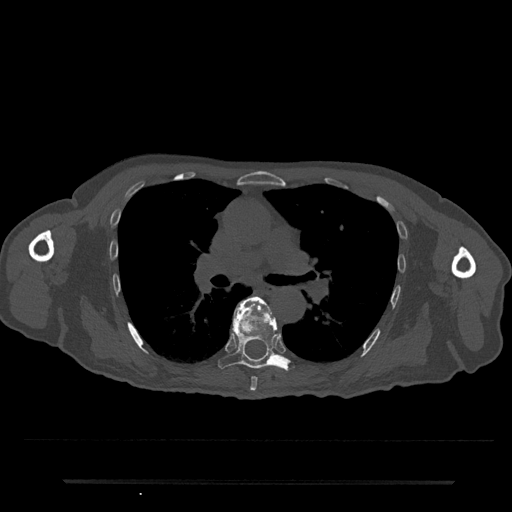
CT including the spine, one axial slice. Position 493 of 797 along the scan axis. Reconstruction kernel Br40s/3. 120 kVp. Bone window (W 1800 / L 400 HU). 0.5 mm slice thickness. 512 × 512 image matrix. Male patient, age 74 years. From the clinical record (not read from this slice): primary cancer: prostate.
Annotated regions visible in this slice (semi-automatically segmented with operator editing):
- T6 vertebra: box from (x=237, y=296) to (x=267, y=391) px
- T7 vertebra: (x=218, y=301)–(x=294, y=371)